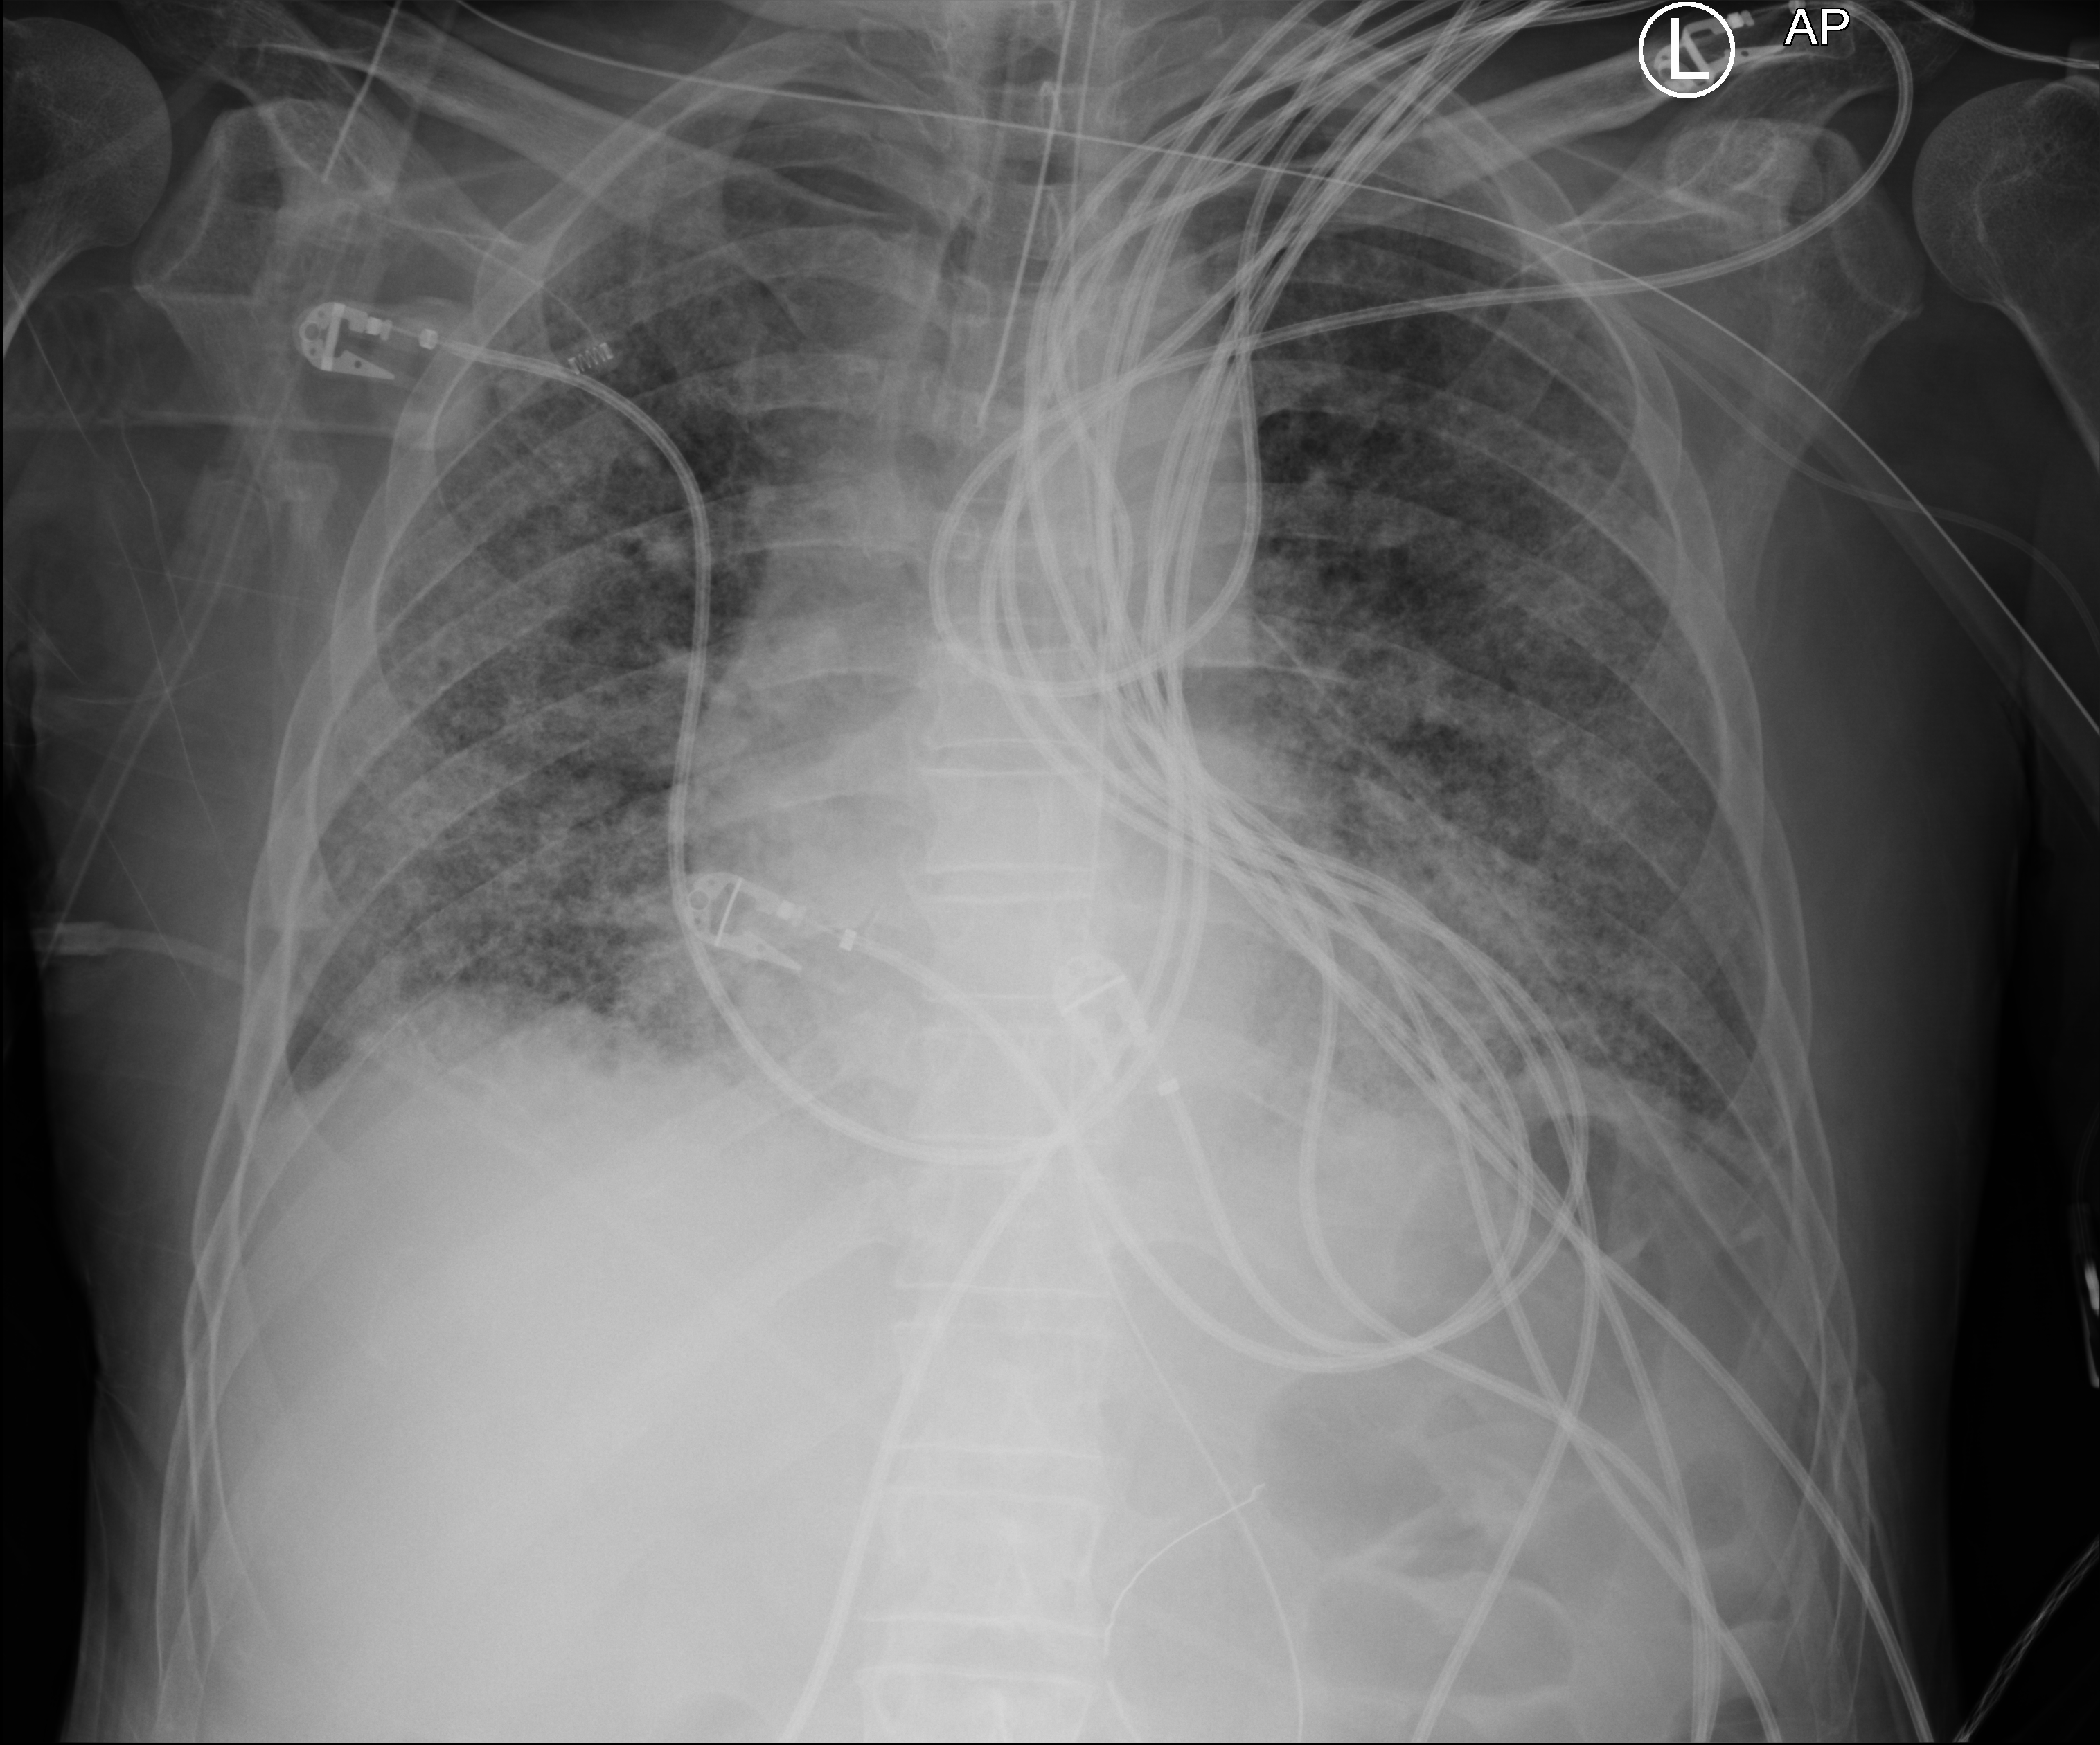
Bedside chest radiograph (computed radiography), anteroposterior (AP) projection. Male patient hospitalised with COVID-19, age 60–74 years.
Hospital-stay facts (about this admission, not read from this image; timing relative to this image not recorded): mechanically ventilated during this hospital stay: yes; admitted to intensive care during this hospital stay: yes.